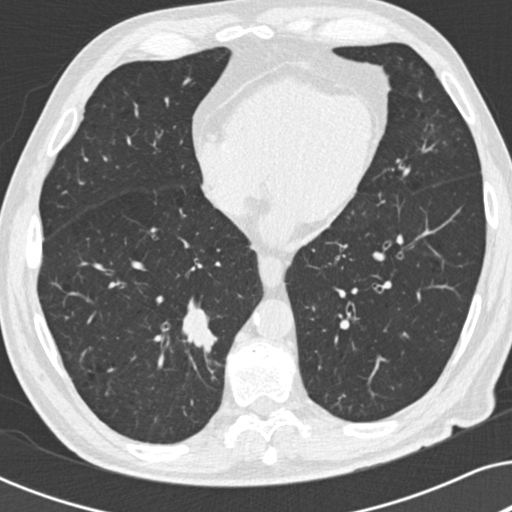
Axial slice from a low-dose chest CT screening exam; baseline screening round; lung window (W 1500 / L -600 HU); 2 mm slice thickness; 120 kVp; slice 108 of 191 in the series. Male participant, aged 73 years at enrolment. Current smoker at enrolment.
- Expert-annotated lung lesion, bounding box (x1, y1, x2, y2) in pixels: (160, 297, 225, 363).
- The screening reader recorded 2 non-calcified nodules or masses ≥4 mm on this exam (right lower lobe, right upper lobe); which of them this box marks is not recorded.
- Lung cancer was diagnosed 63 days after this screen: carcinoid tumor, NOS, right lower lobe, carcinoid, stage not assessed, 12 mm at pathology.